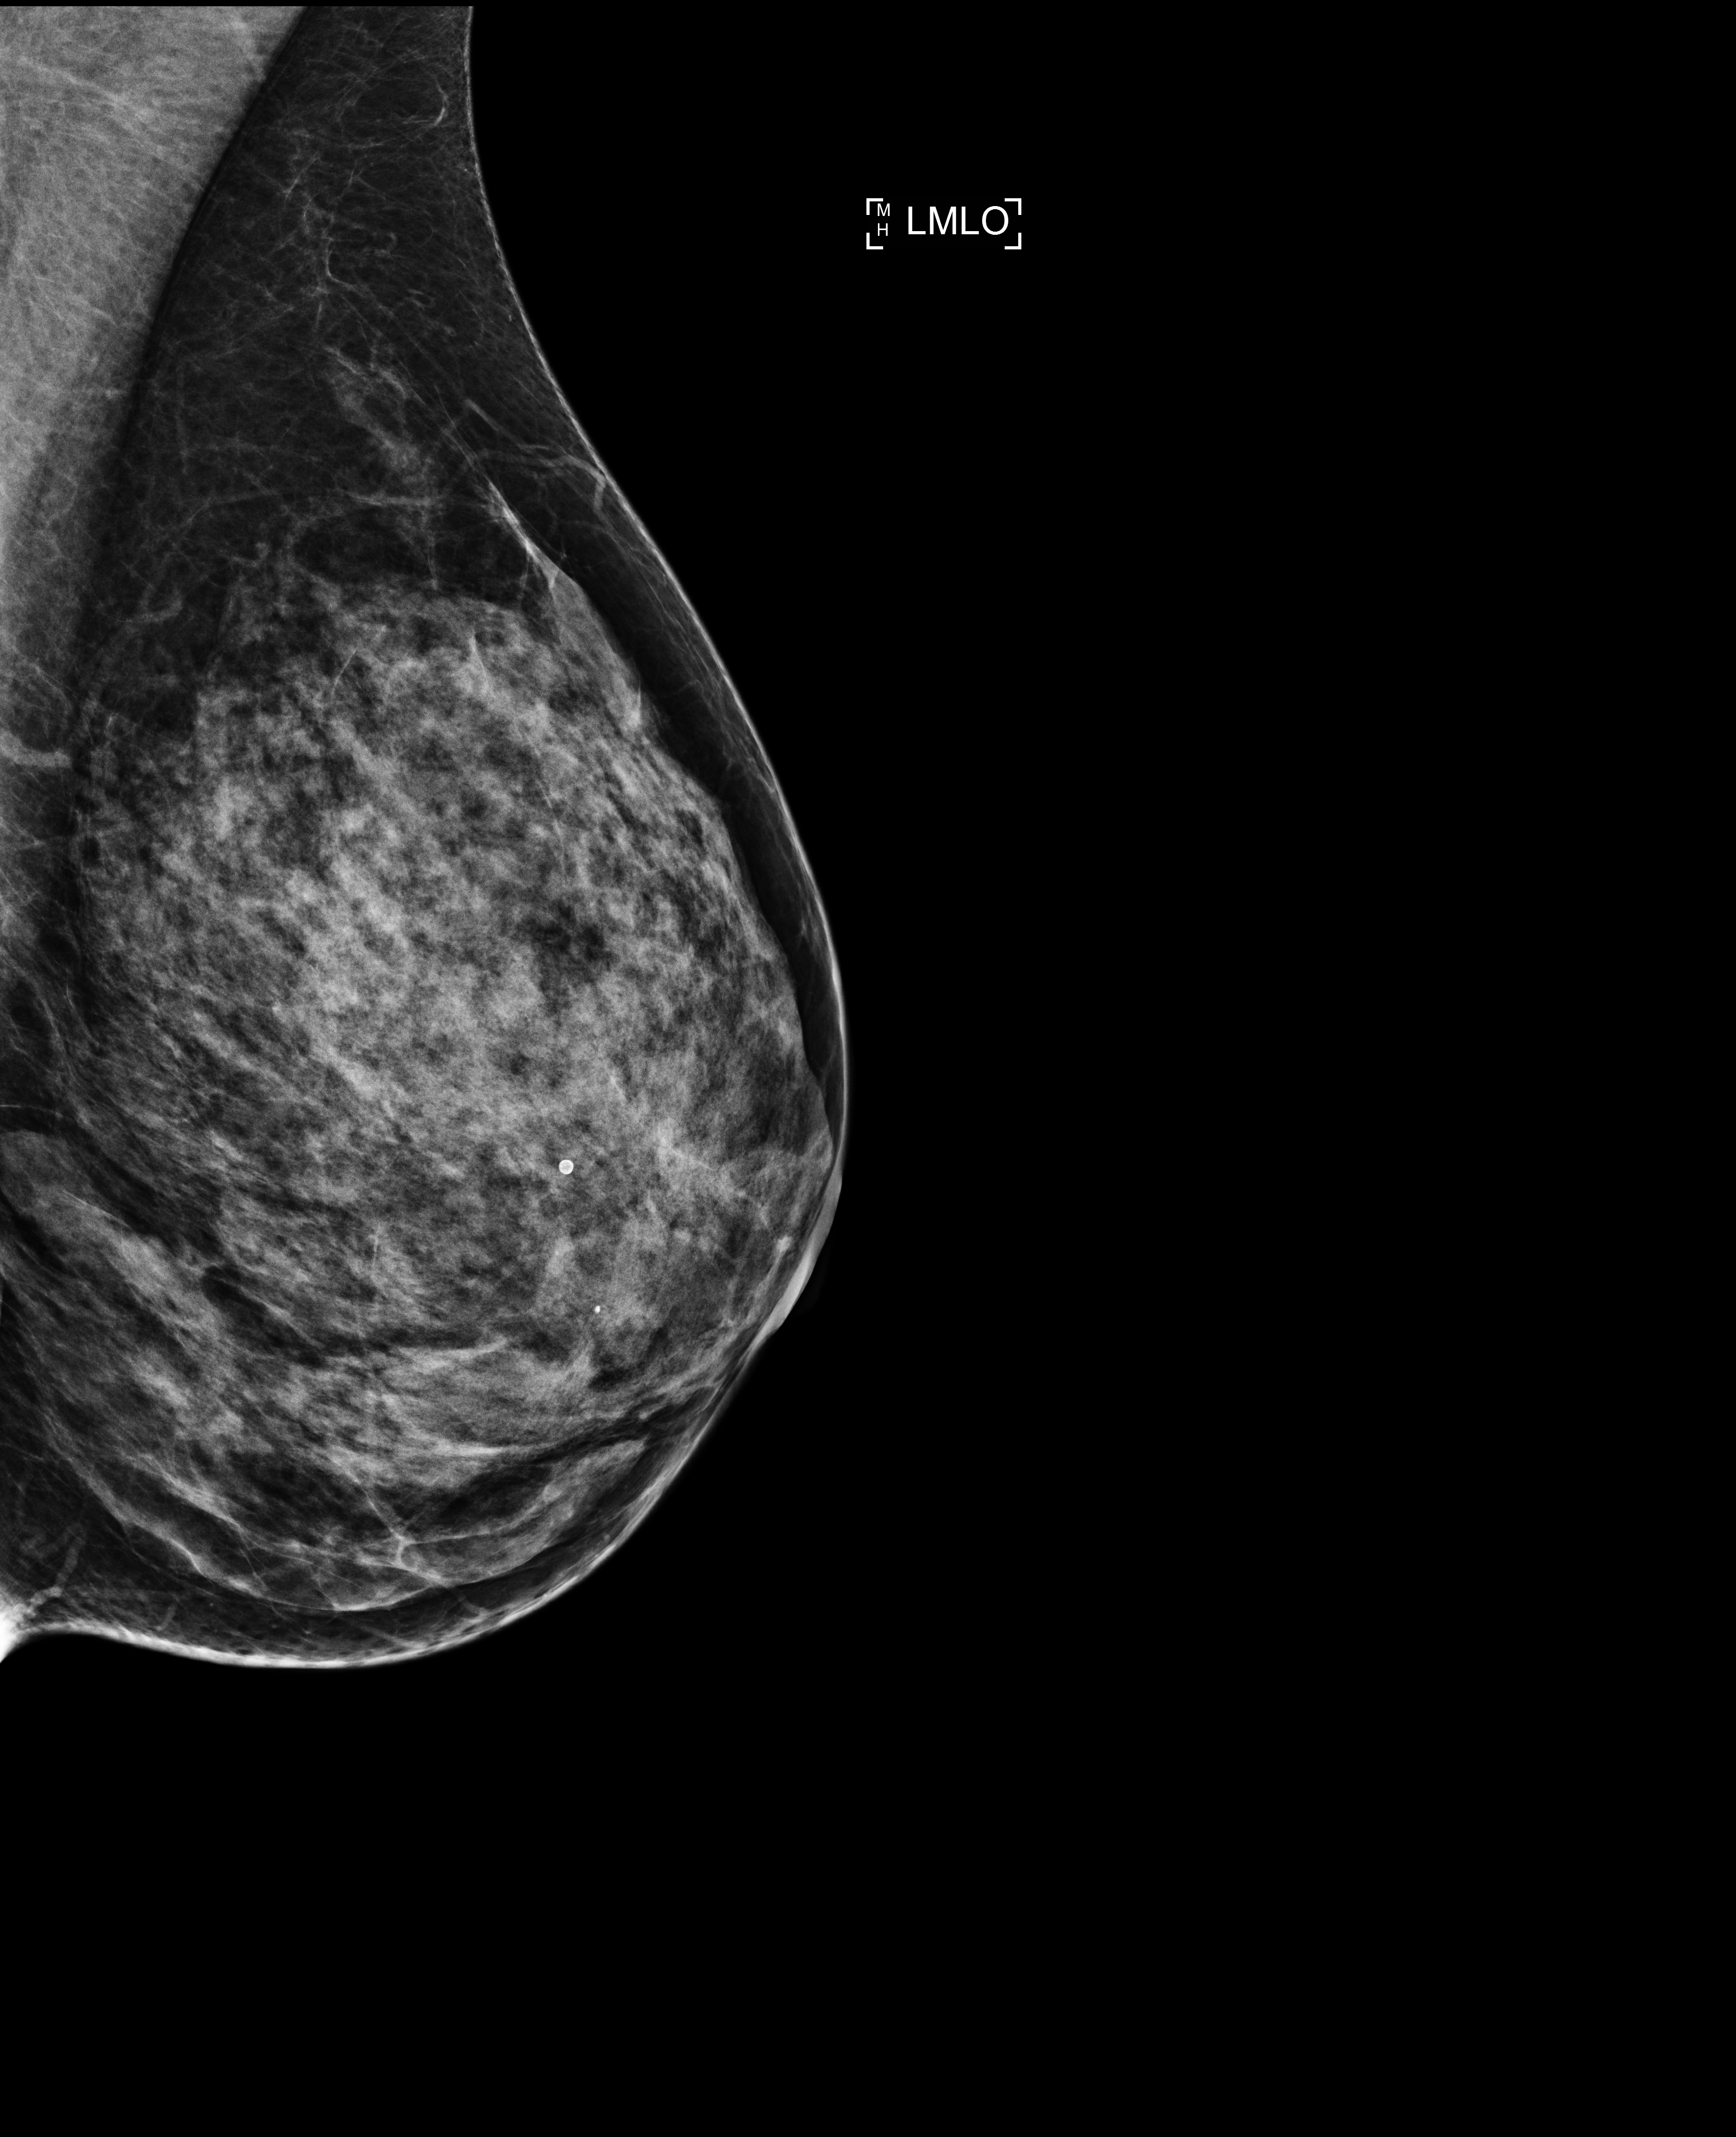
Annual screening mammography examination. Patient: female, 41 years.
Image type: full-field digital mammogram. Breast: left. Projection: MLO view.